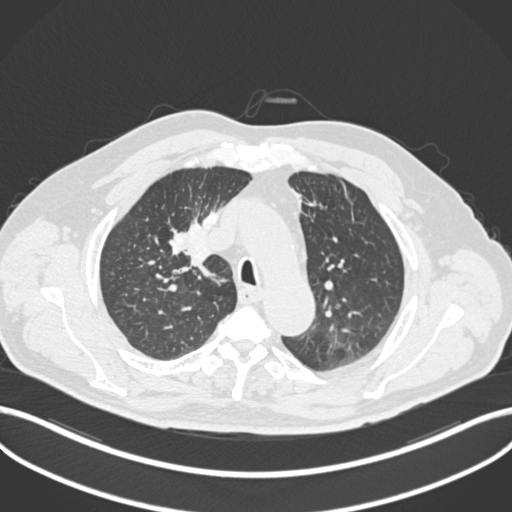
Chest CT, one axial slice. Reconstruction kernel B30f. 120 kVp. Lung window (W 1500 / L -600 HU). 512 × 512 image matrix. Male patient, age 60 years. From the clinical record (not read from this slice): clinical TNM (as recorded): T1b N1 M0.
Annotated regions visible in this slice (bounding box drawn by a radiologist):
- lung tumour (recorded histology: squamous cell carcinoma): box from (x=169, y=205) to (x=210, y=272) px